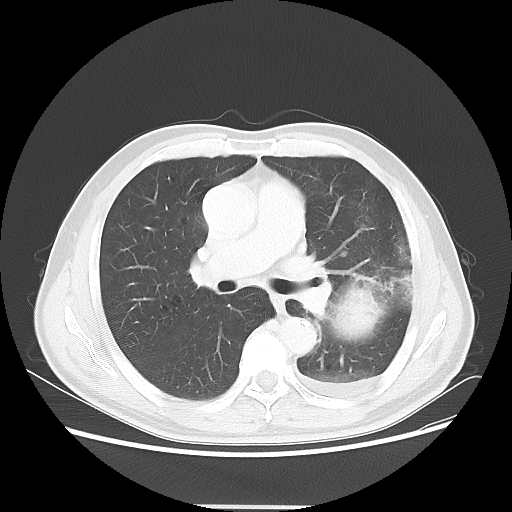
Chest CT, one axial slice. Slice 31 of 53 in the series (ordered by position). Reconstruction kernel LUNG. 100 kVp. Lung window (W 1500 / L -600 HU). 5 mm slice thickness. 512 × 512 image matrix. Male patient, age 60 years. Case-level facts recorded for this patient, not image findings: clinical TNM (as recorded): T4 N1 M1a.
Annotated regions visible in this slice (bounding box drawn by a radiologist):
- lung tumour (recorded histology: large cell carcinoma): bounding box <328,265,405,351> (left, top, right, bottom; pixels)